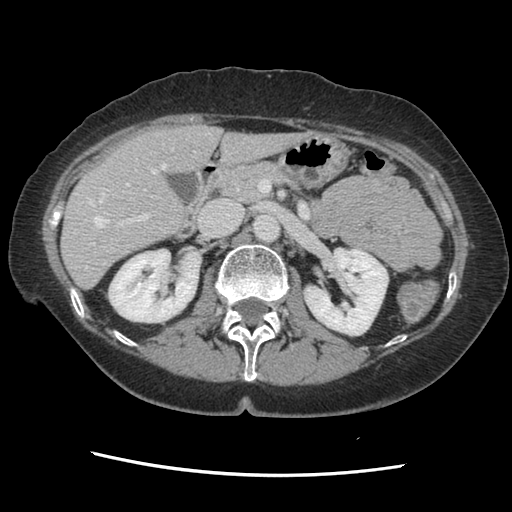
Contrast-enhanced abdominal CT, one axial slice. Position 72 of 141 along the scan axis. 120 kVp. Soft-tissue window (W 400 / L 40 HU). 2.5 mm slice thickness. 512 × 512 image matrix. Female patient, age 61 years. Case-level facts recorded for this patient, not image findings: diagnosis: colorectal cancer liver metastases, imaged before liver resection; multiple liver metastases: no; largest metastasis: 2.4 cm; disease in both lobes: no.
Outlined on this slice (outlined manually by an expert reader):
- hepatic veins: bounding box (x1, y1, x2, y2) in pixels: (85, 149, 173, 269)
- liver: (62, 126, 298, 288)
- planned liver remnant (the part of the liver to remain after resection): (62, 126, 298, 288)
- portal vein (with intrahepatic branches): (92, 183, 149, 245)